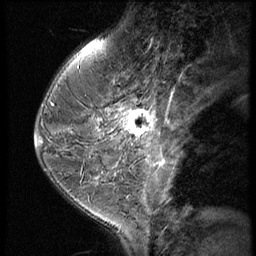
Breast MRI (dynamic contrast-enhanced), one sagittal slice. Slice 22 of 60 in the series (ordered by position). 3 images stored at this slice position (order not interpretable as contrast timing). 1.5 T. TE 4.2 ms, TR 9 ms. 2.5 mm slice thickness. 256 × 256 image matrix, field of view 180 × 180 mm. Patient: female, 38 years. Case-level facts recorded for this patient, not image findings: setting: breast cancer imaged before/during neoadjuvant chemotherapy; receptor status: triple-negative.
Outlined on this slice (semi-automatically segmented with operator editing):
- analysis volume of interest (the breast-tissue region the enhancement analysis was run in; not a lesion): bounding box <119,93,165,150> (left, top, right, bottom; pixels)
- tumour enhancement mask (voxels above the 140 % enhancement threshold inside the analysis volume of interest): <119,107,156,139>